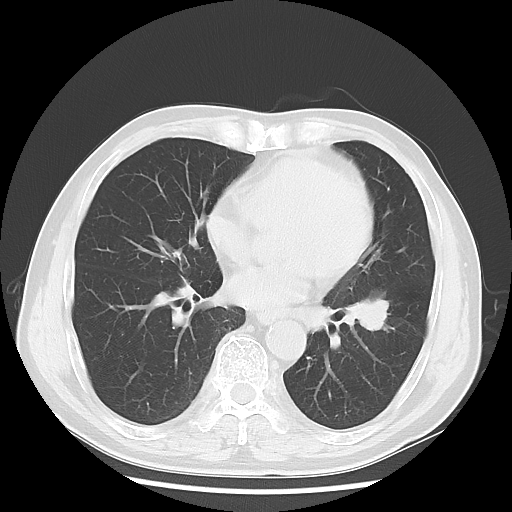
Chest CT, one axial slice; position 29 of 68 along the scan axis; reconstruction kernel LUNG; 120 kVp; lung window (W 1500 / L -600 HU); 5 mm slice thickness; 512 × 512 image matrix, field of view 360 × 360 mm. Patient: male, 71 years. Case-level facts recorded for this patient, not image findings: clinical TNM (as recorded): T1c N1 M0; histopathological grade: G2-3.
Outlined on this slice (rectangle marked by the reading radiologist):
- lung tumour (recorded histology: adenocarcinoma): bounding box <345,295,403,336> (left, top, right, bottom; pixels)